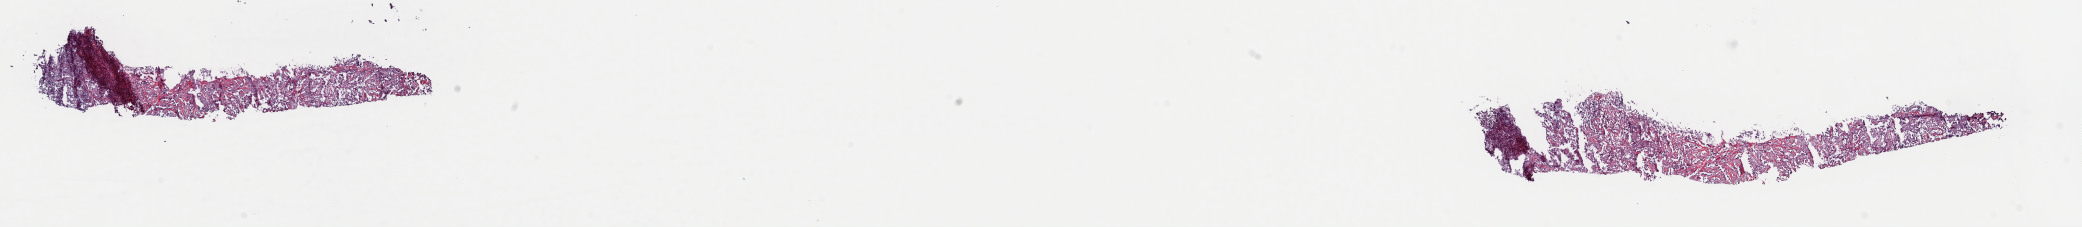
Whole-slide histology image, Hematoxylin and eosin (H&E) stained — whole scanned area (about 32.9 x 3.6 mm) shown as a low-resolution overview. Frozen section from the top of the tissue portion. Mesothelium, primary tumour sample. Patient: female, age at initial diagnosis 73 years. Slide review estimates, as recorded: tumour cells 70%, tumour nuclei 70%, normal cells 0%, stromal cells 20%, necrosis 10%. Inflammatory infiltration, as recorded: lymphocyte infiltration 40%, monocyte infiltration 20%, neutrophil infiltration 20%.
Histologic diagnosis: Epithelioid mesothelioma, malignant (pleura, NOS). AJCC pathologic stage: III (6th edition). Laterality: right.